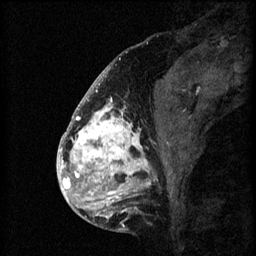
Breast MRI (dynamic contrast-enhanced), one sagittal slice; position 26 of 60 along the scan axis; 3 images stored at this slice position (order not interpretable as contrast timing); 1.5 T; TE 4.2 ms, TR 8.2 ms; 2 mm slice thickness; 256 × 256 image matrix, field of view 180 × 180 mm. Female patient, age 41 years.
Annotated regions visible in this slice (semi-automatically segmented with operator editing):
- analysis volume of interest (the breast-tissue region the enhancement analysis was run in; not a lesion): box from (x=72, y=108) to (x=176, y=205) px
- tumour enhancement mask (voxels above the 70 % enhancement threshold inside the analysis volume of interest): (x=72, y=108)–(x=152, y=205)